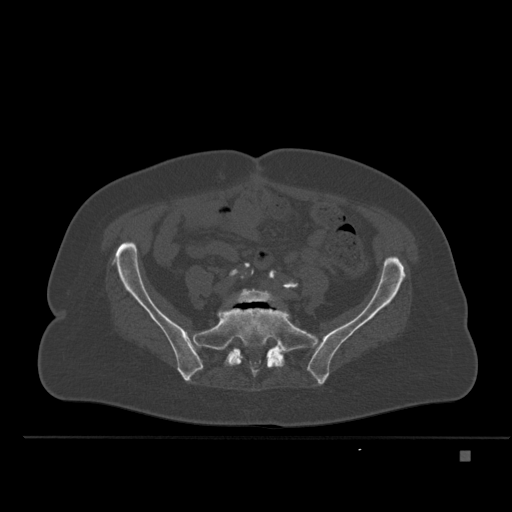
CT including the spine, one axial slice; slice 147 of 477 in the series (ordered by position); bone window (W 1800 / L 400 HU); 512 × 512 image matrix, field of view 422 × 422 mm. Female patient, age 74 years. From the clinical record (not read from this slice): primary cancer: colon.
Outlined on this slice (semi-automatically segmented with operator editing):
- L5 vertebra: box from (x=235, y=288) to (x=277, y=304) px